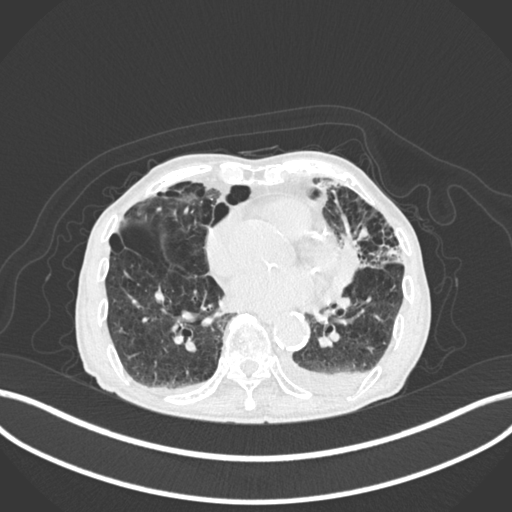
Chest CT, one axial slice. Position 79 of 400 along the scan axis. Lung window (W 1500 / L -600 HU). 1 mm slice thickness. 512 × 512 image matrix, field of view 400 × 400 mm. Patient: male, 90 years or older. From the clinical record (not read from this slice): clinical TNM (as recorded): T2b N1 M0.
Structures marked on this image (rectangle marked by the reading radiologist):
- lung tumour (recorded histology: squamous cell carcinoma): bounding box <338,231,367,294> (left, top, right, bottom; pixels)